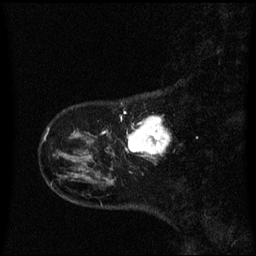
Breast MRI (dynamic contrast-enhanced), one sagittal slice. Slice 10 of 60 in the series (ordered by position). Dynamic contrast-enhanced series, image 2 of 3 at this slice position (ordered by acquisition). 1.5 T. TE 4.2 ms, TR 8.4 ms. 2 mm slice thickness. 256 × 256 image matrix, field of view 220 × 220 mm. Female patient, age 41 years. From the clinical record (not read from this slice): setting: breast cancer imaged before/during neoadjuvant chemotherapy; receptor status: triple-negative.
Structures marked on this image (semi-automatic segmentation, software-assisted and operator-edited):
- analysis volume of interest (the breast-tissue region the enhancement analysis was run in; not a lesion): box from (x=121, y=104) to (x=169, y=157) px
- tumour enhancement mask (voxels above the 70 % enhancement threshold inside the analysis volume of interest): (x=129, y=118)–(x=169, y=155)